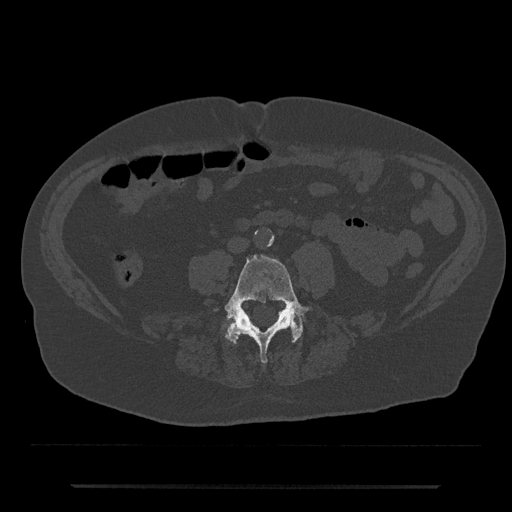
CT including the spine, one axial slice; position 346 of 797 along the scan axis; reconstruction kernel Br40s/3; bone window (W 1800 / L 400 HU); 0.5 mm slice thickness; 512 × 512 image matrix, field of view 434 × 434 mm. Male patient, age 80 years. Case-level facts recorded for this patient, not image findings: primary cancer: prostate.
Outlined on this slice (semi-automatically segmented with operator editing):
- L4 vertebra: box from (x=224, y=255) to (x=314, y=363) px
- L5 vertebra: (x=227, y=317)–(x=302, y=342)